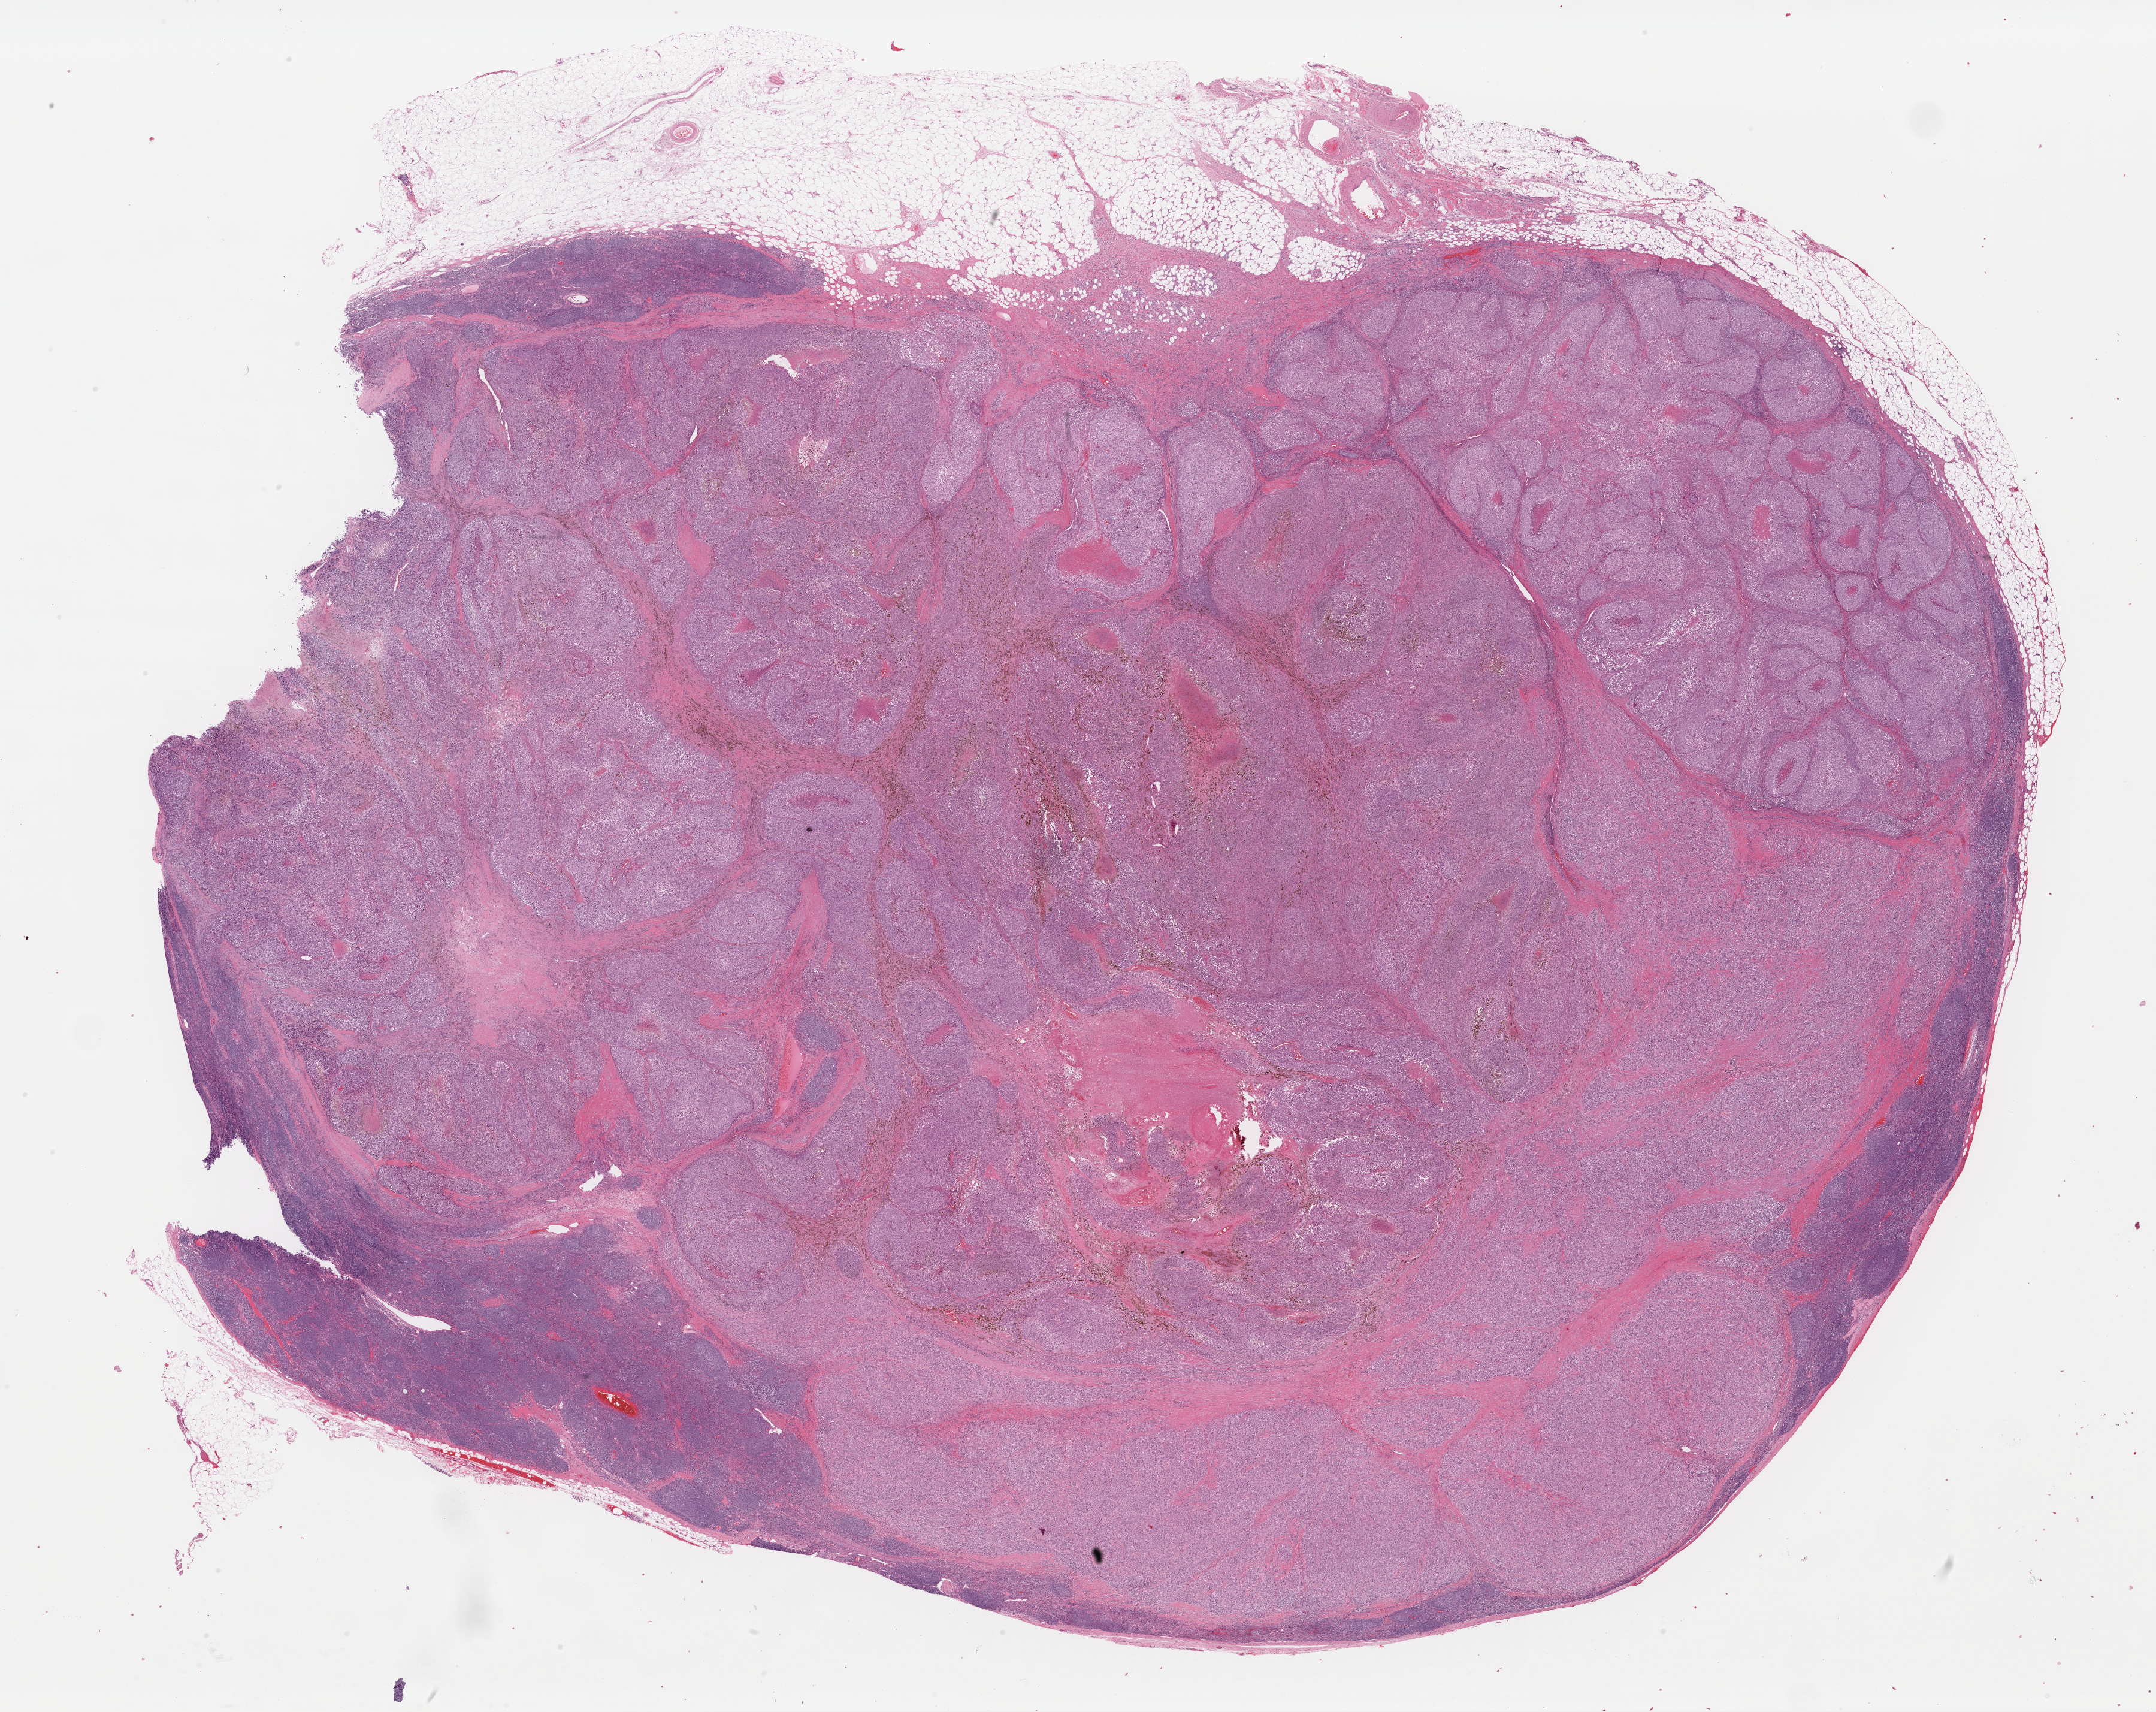
Whole-slide histology image, Hematoxylin and eosin (H&E) stained — low-resolution overview of the scanned area, about 28.4 x 22.6 mm, formalin-fixed paraffin-embedded (FFPE) diagnostic section, primary tumour sample from the skin. Patient: male, age at initial diagnosis 49 years.
Diagnosis: Malignant melanoma, NOS.